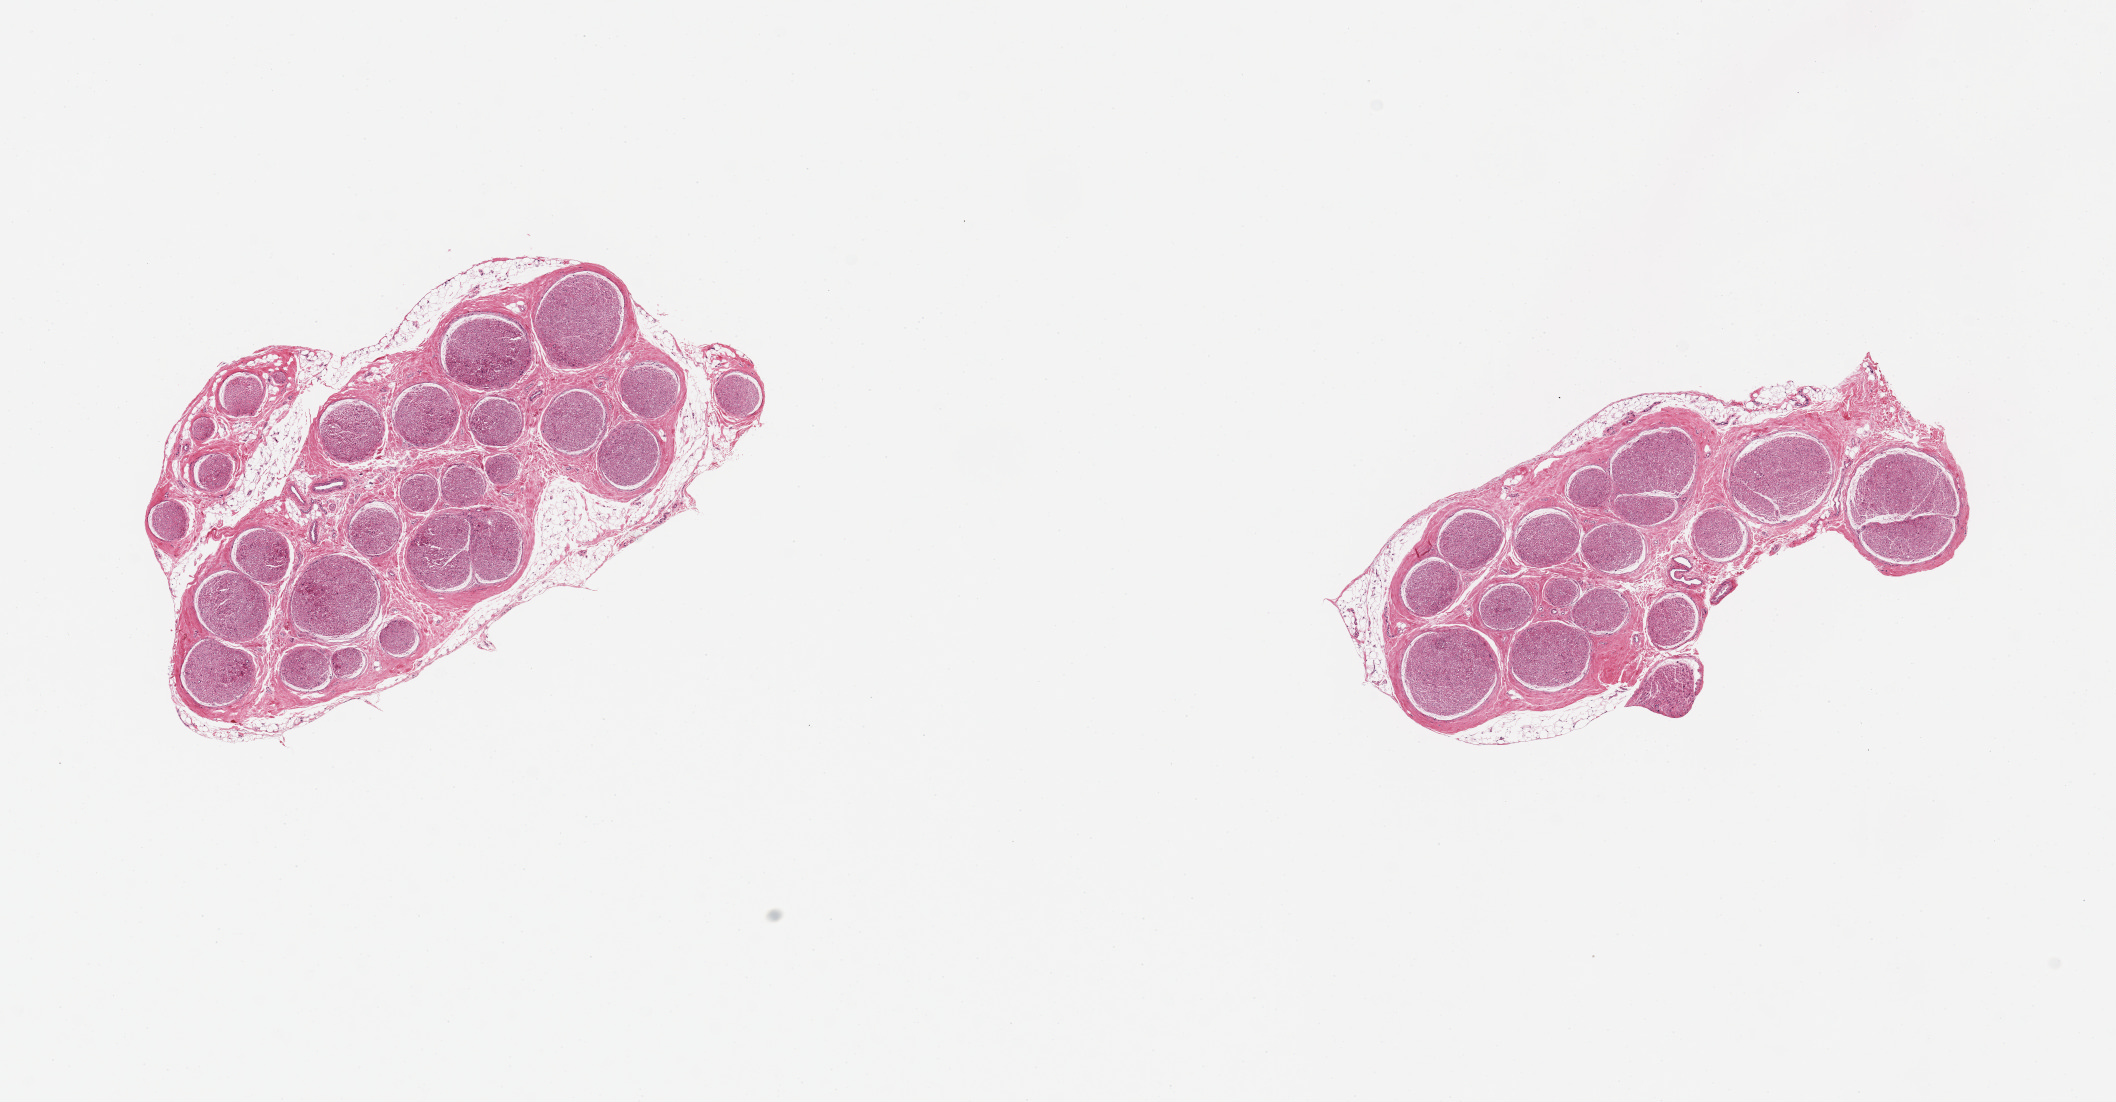
Whole-slide image, haematoxylin and eosin stain, shown as a low-resolution overview of the whole scanned area (about 16.7 x 8.7 mm). PAXgene-fixed paraffin-embedded (PFPE) section. Target tissue: tibial nerve. Tissue donor sample. Donor sex: female.
Pathologist's review note for this sample: 2 pieces ~4mm d. Reasonably clean specimens, discontinuous rim of adherent fat up to ~0.2-0.3mm.